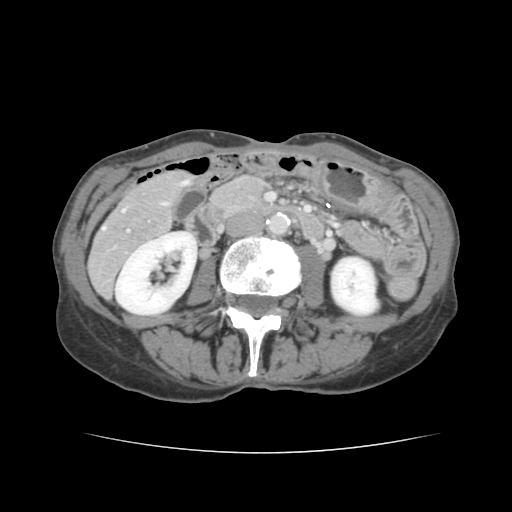
Contrast-enhanced abdominal CT, one axial slice; slice 41 of 136 in the series (ordered by position); intravenous contrast given; soft-tissue window (W 400 / L 40 HU); 2.5 mm slice thickness; 512 × 512 image matrix. Female patient, age 77 years. Case-level facts recorded for this patient, not image findings: diagnosis: colorectal cancer liver metastases, imaged before liver resection; multiple liver metastases: yes; largest metastasis: 3 cm; chemotherapy before resection: yes.
Structures marked on this image (outlined manually by an expert reader):
- hepatic veins: bounding box <103,181,188,230> (left, top, right, bottom; pixels)
- liver: <89,172,187,294>